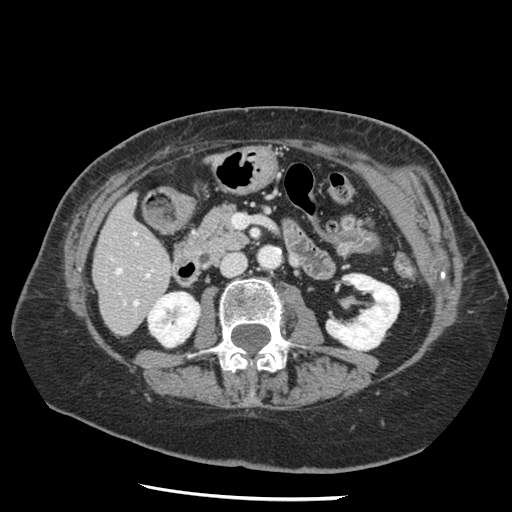
Contrast-enhanced abdominal CT, one axial slice. Position 49 of 148 along the scan axis. Intravenous contrast given. Soft-tissue window (W 400 / L 40 HU). 512 × 512 image matrix. Female patient, age 85 years. From the clinical record (not read from this slice): diagnosis: colorectal cancer liver metastases, imaged before liver resection.
Outlined on this slice (manually delineated by an expert):
- hepatic veins: bounding box [x1, y1, x2, y2] px = [116, 269, 138, 305]
- liver: [94, 197, 173, 334]
- planned liver remnant (the part of the liver to remain after resection): [95, 197, 173, 333]